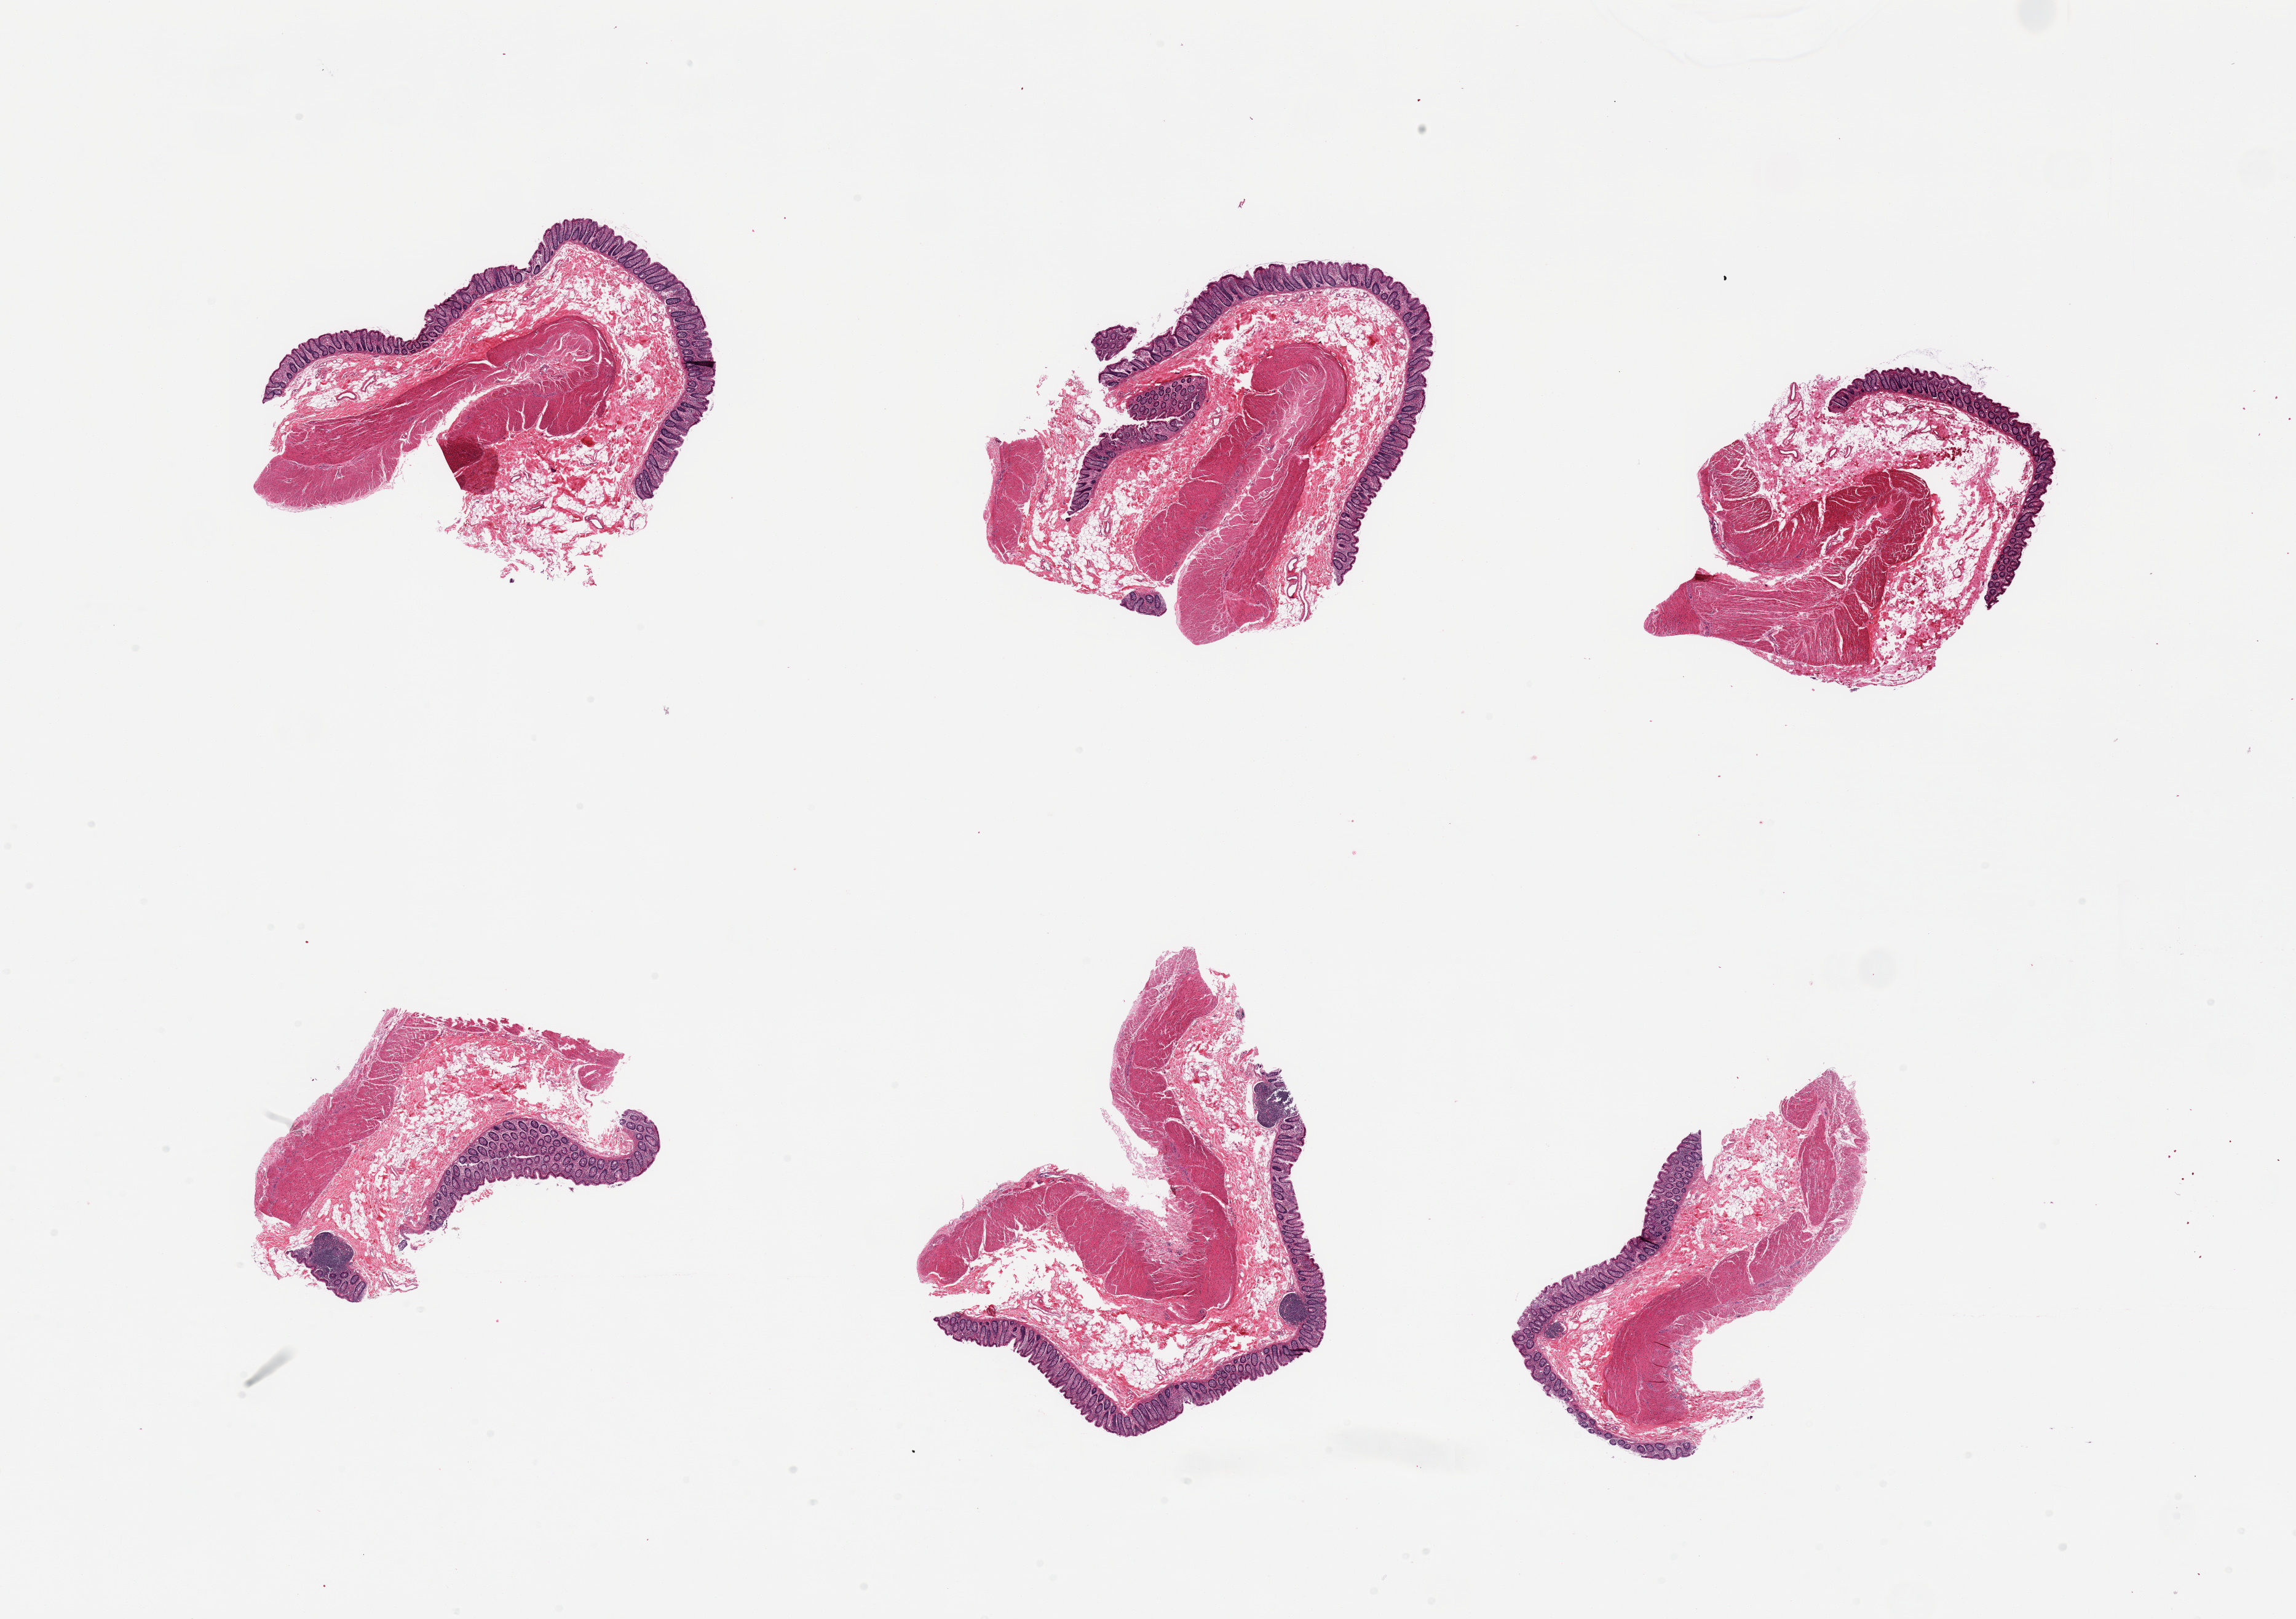
Haematoxylin and eosin whole-slide image, shown as a low-resolution overview of the whole scanned area (about 29.5 x 20.8 mm, from a 20x scan). PAXgene-fixed paraffin-embedded (PFPE) section. Section of transverse colon (target tissue). Tissue donor sample. Donor: female.
• review note (as recorded): 6 pieces, mucosa well preserved, ~0.3mm, ~10-15% thickness